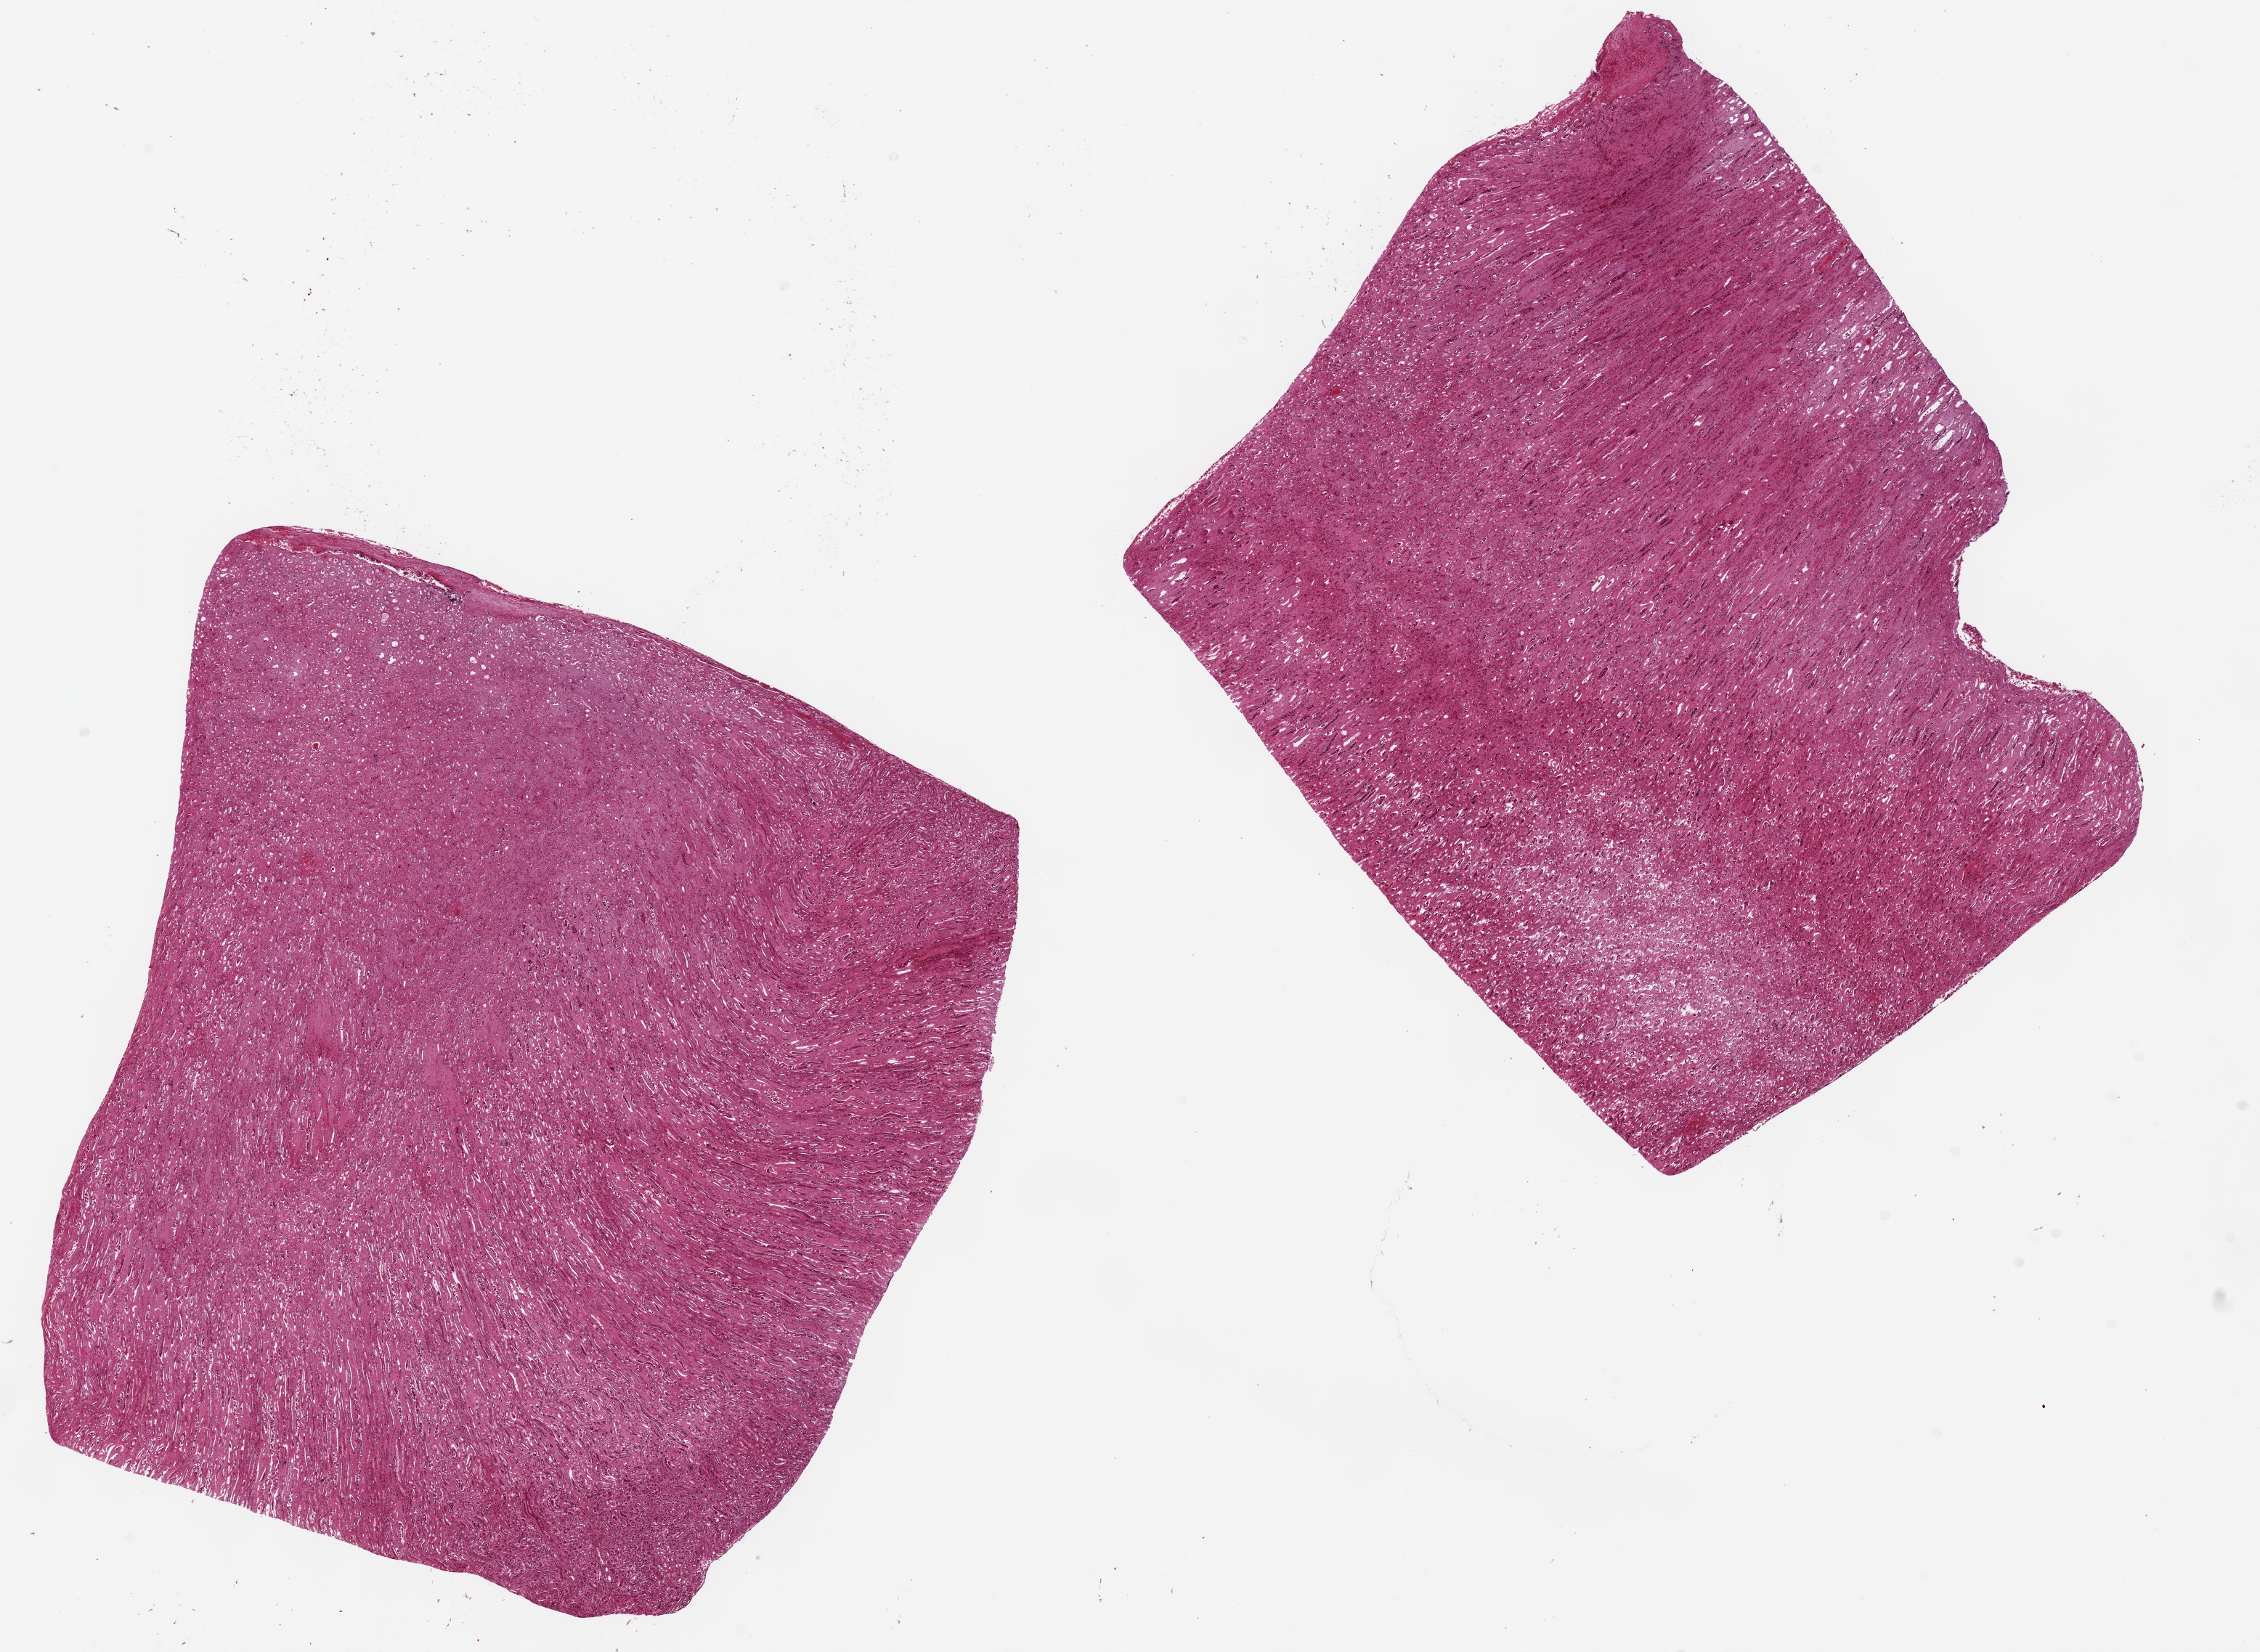
Digitized hematoxylin and eosin (H&E)-stained section, whole scanned area (about 24.6 x 18.0 mm, from a 20x scan) shown as a low-resolution overview, PAXgene-fixed, paraffin-embedded tissue, target tissue: renal medulla, tissue donor sample. Donor sex: female.
Reviewer comment on this tissue sample: 2 ~10x9mm aliquots. Tubules badly autolyzed.